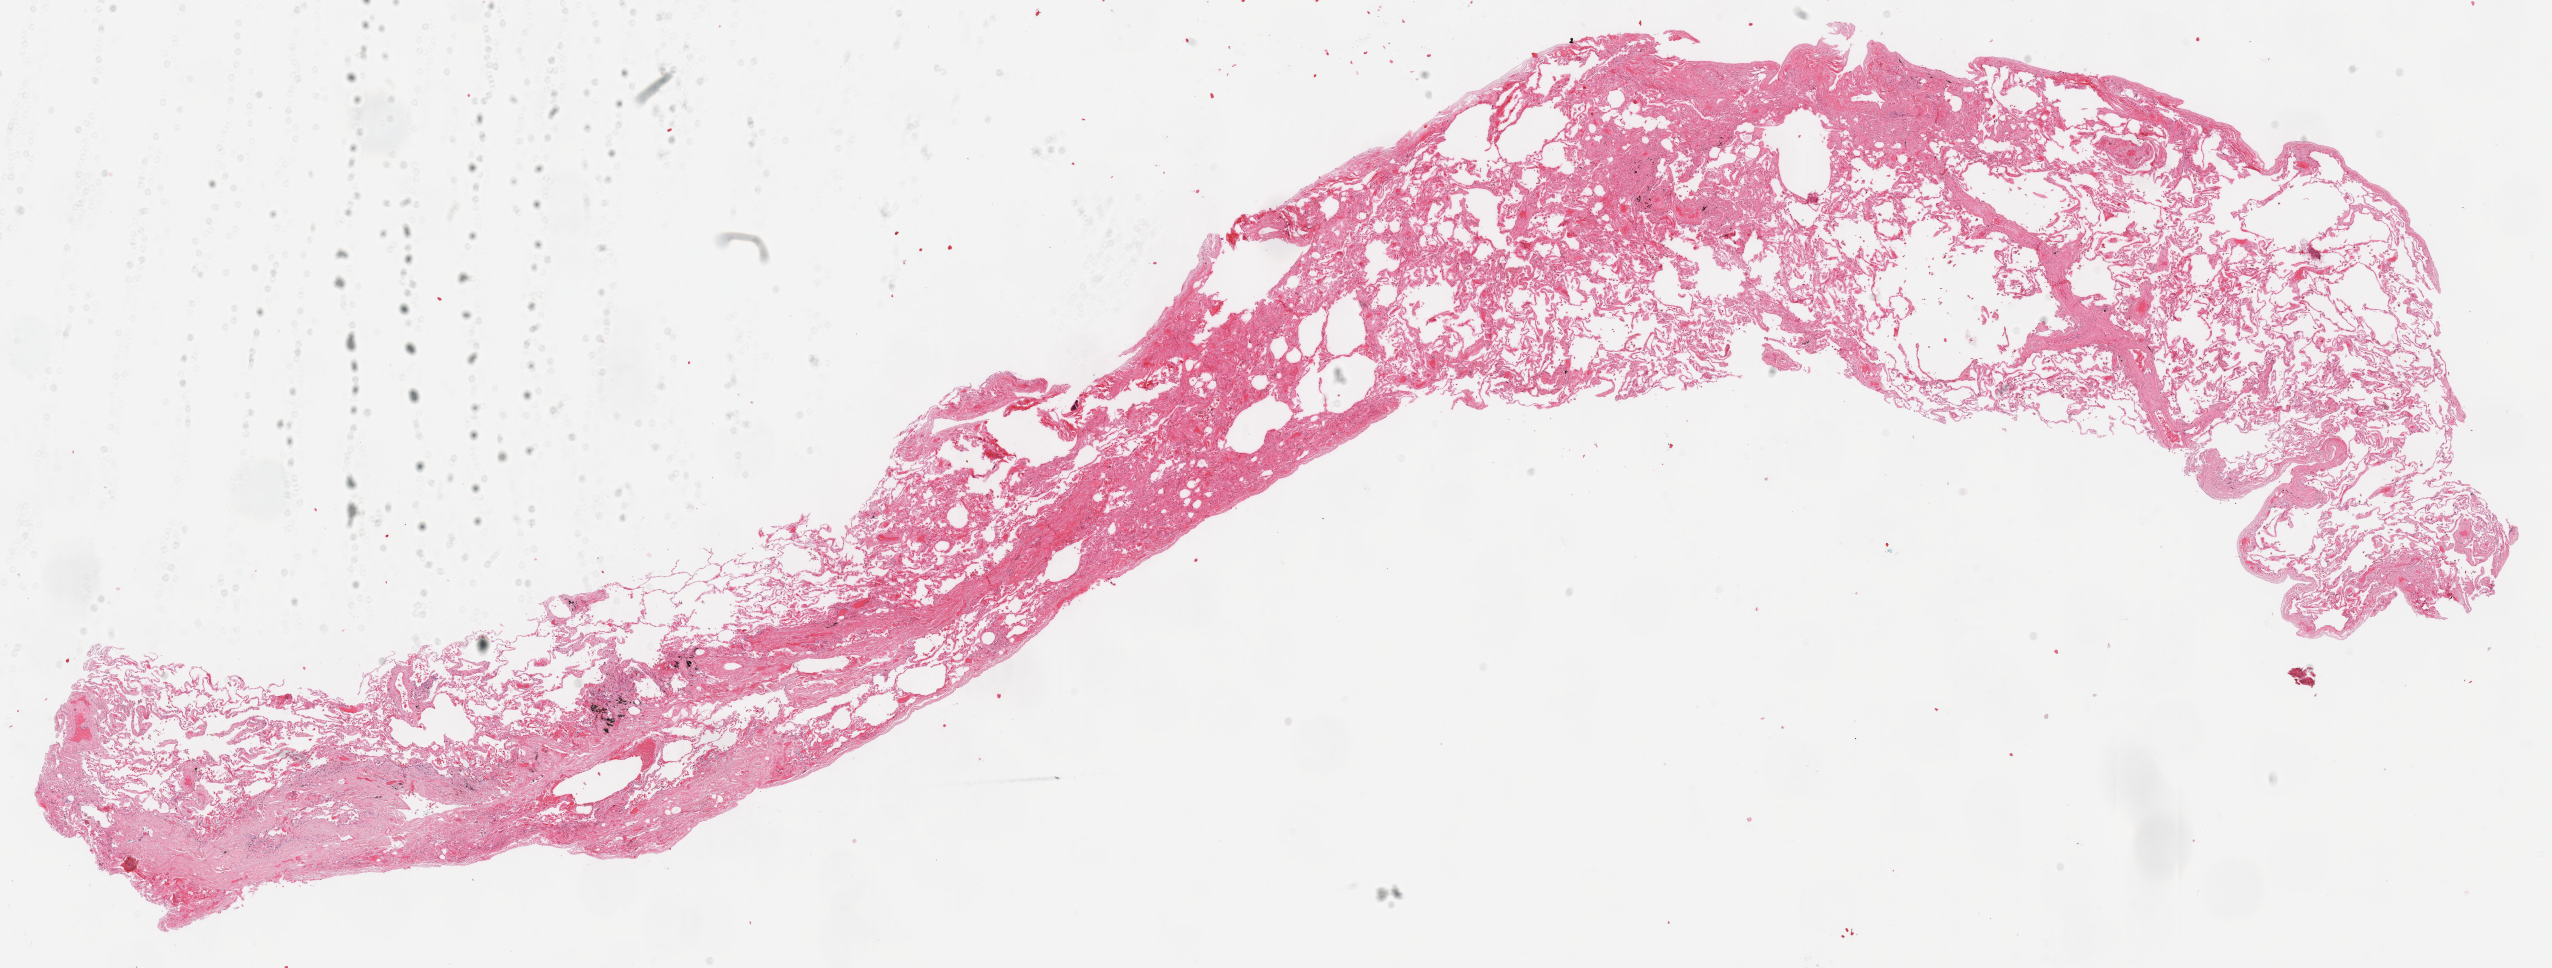
H&E-stained whole-slide image, a low-resolution overview of the entire scanned area, about 20.1 x 7.6 mm; frozen section from the top of the tissue portion; solid tissue normal (non-tumour tissue) sample from the lung. Female, age 50 years at initial diagnosis.
This section: solid tissue normal (non-tumour) sample from the same patient. Patient diagnosis: Adenocarcinoma, NOS.